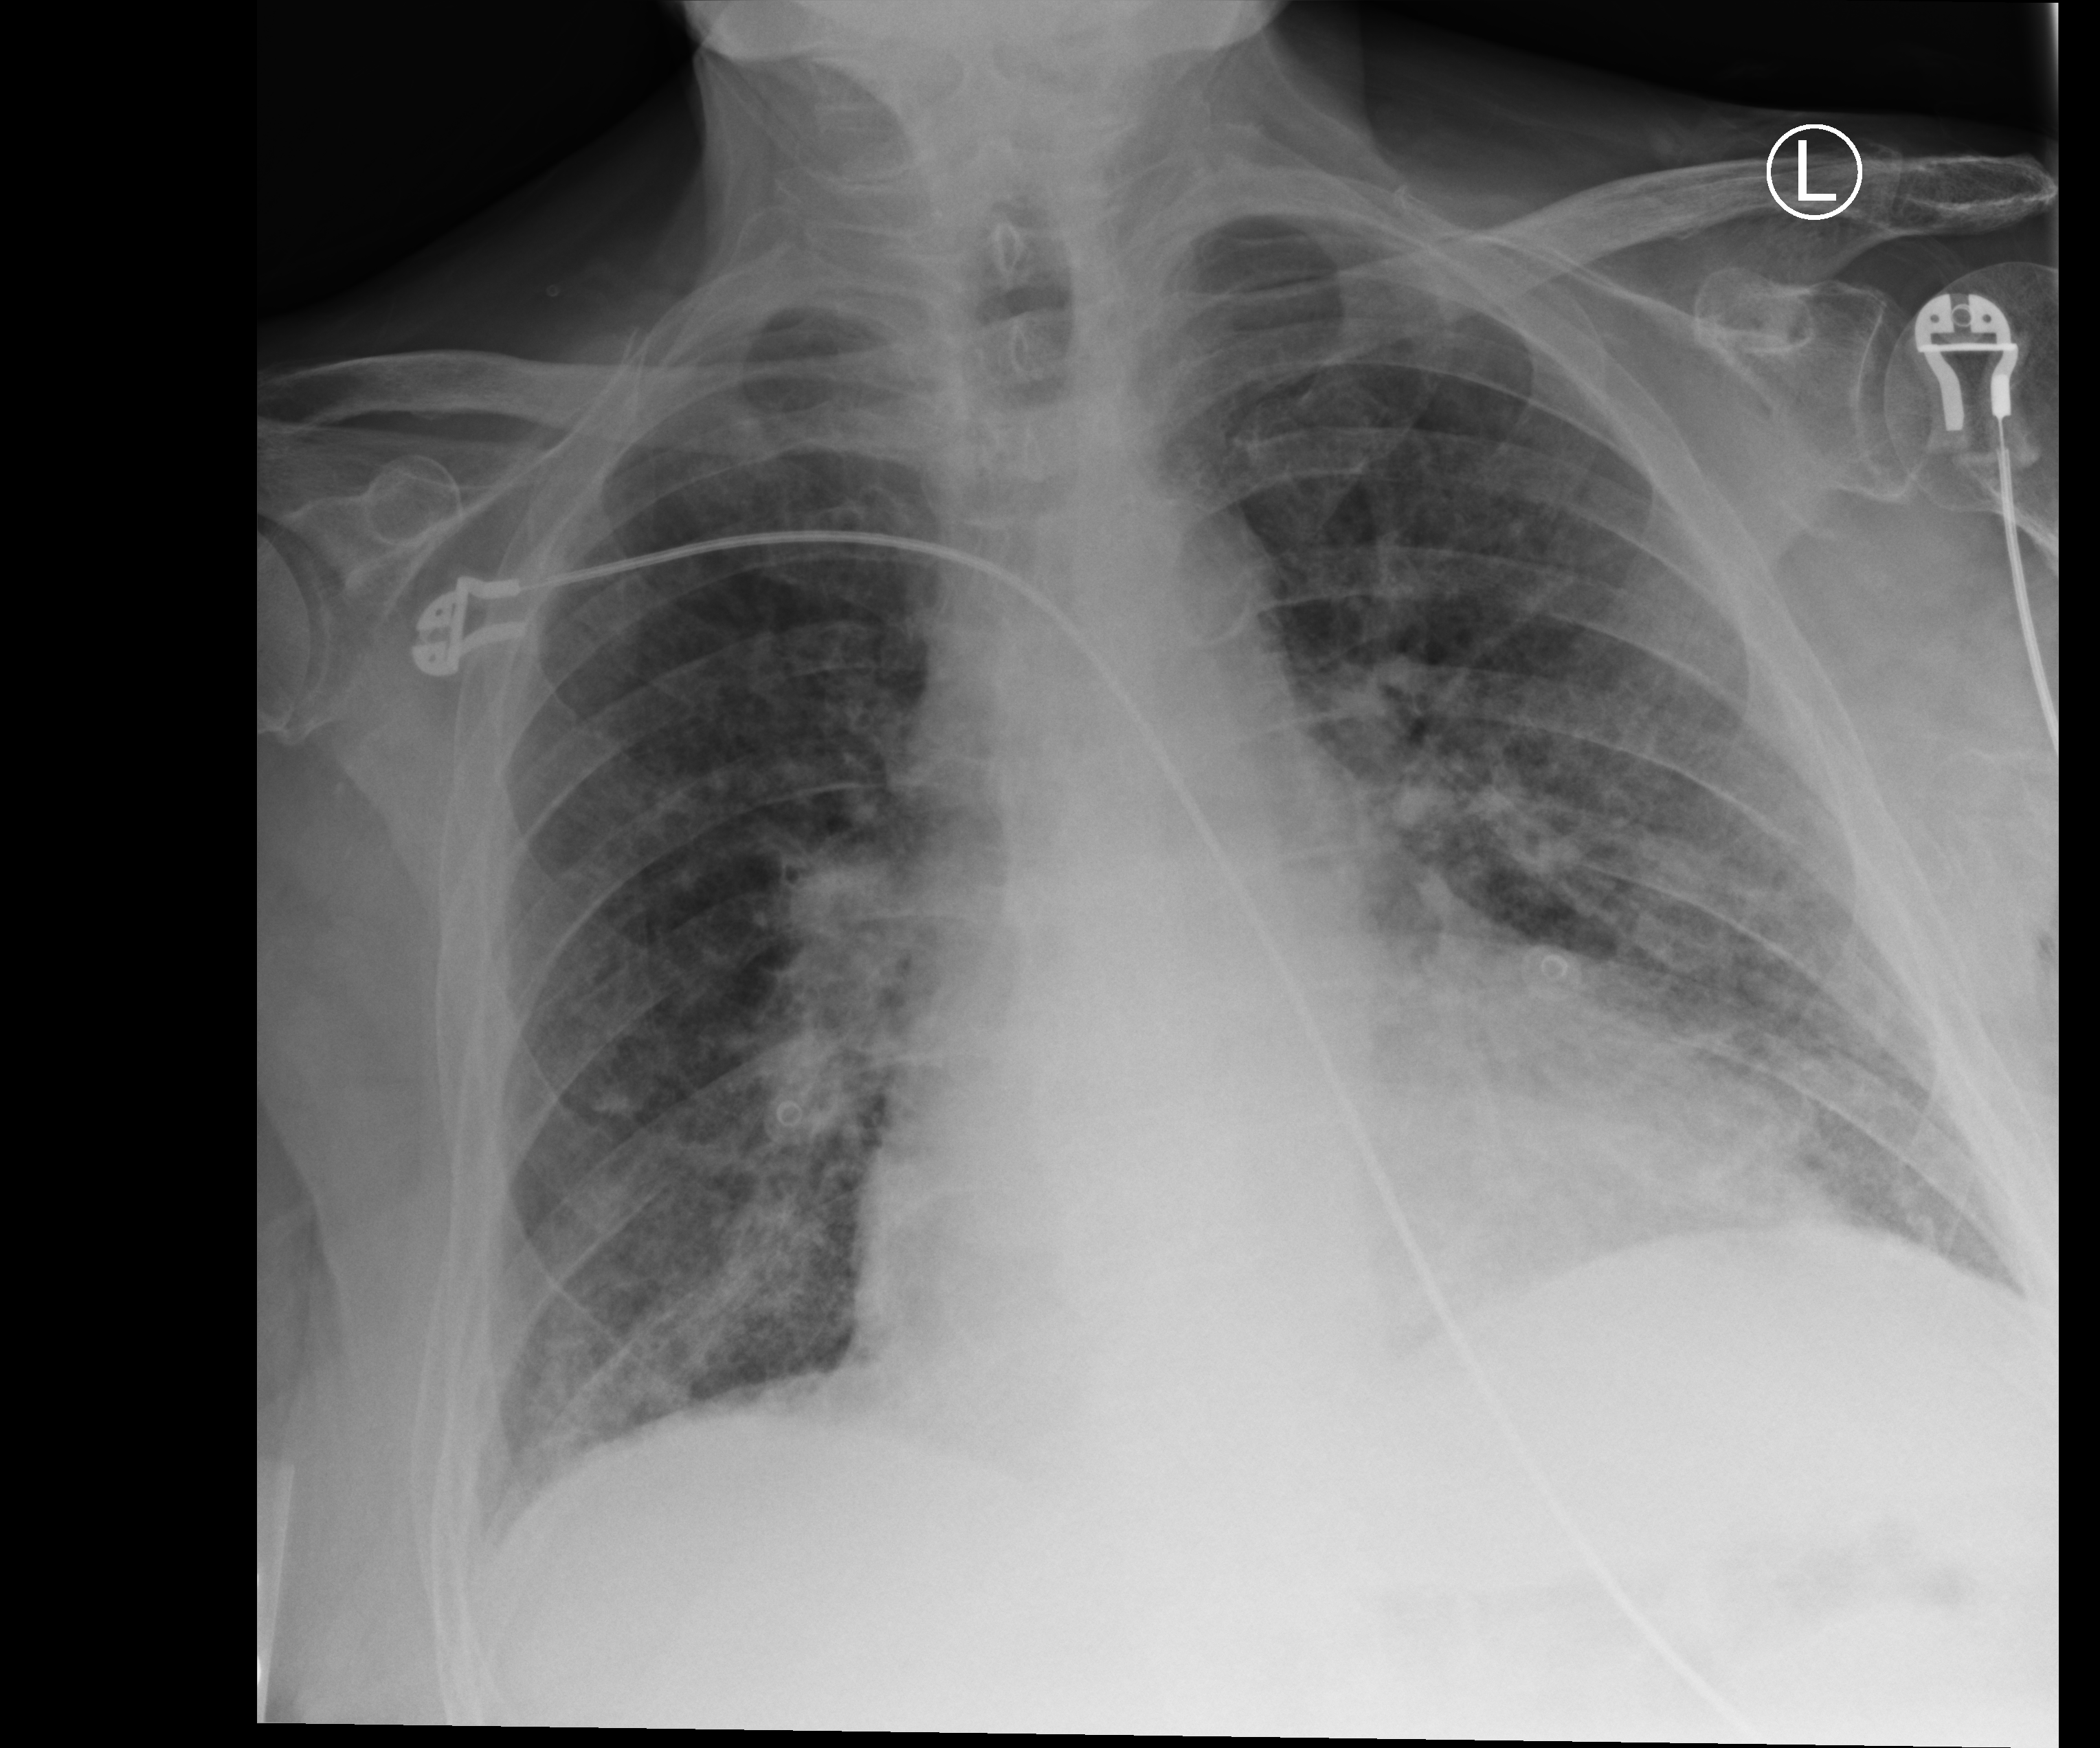
Portable chest radiograph, anteroposterior (AP) projection. Patient hospitalised with COVID-19; male, aged 75–90 years.
Hospital-stay facts (about this admission, not read from this image; timing relative to this image not recorded): chronic kidney disease (admission record): yes.